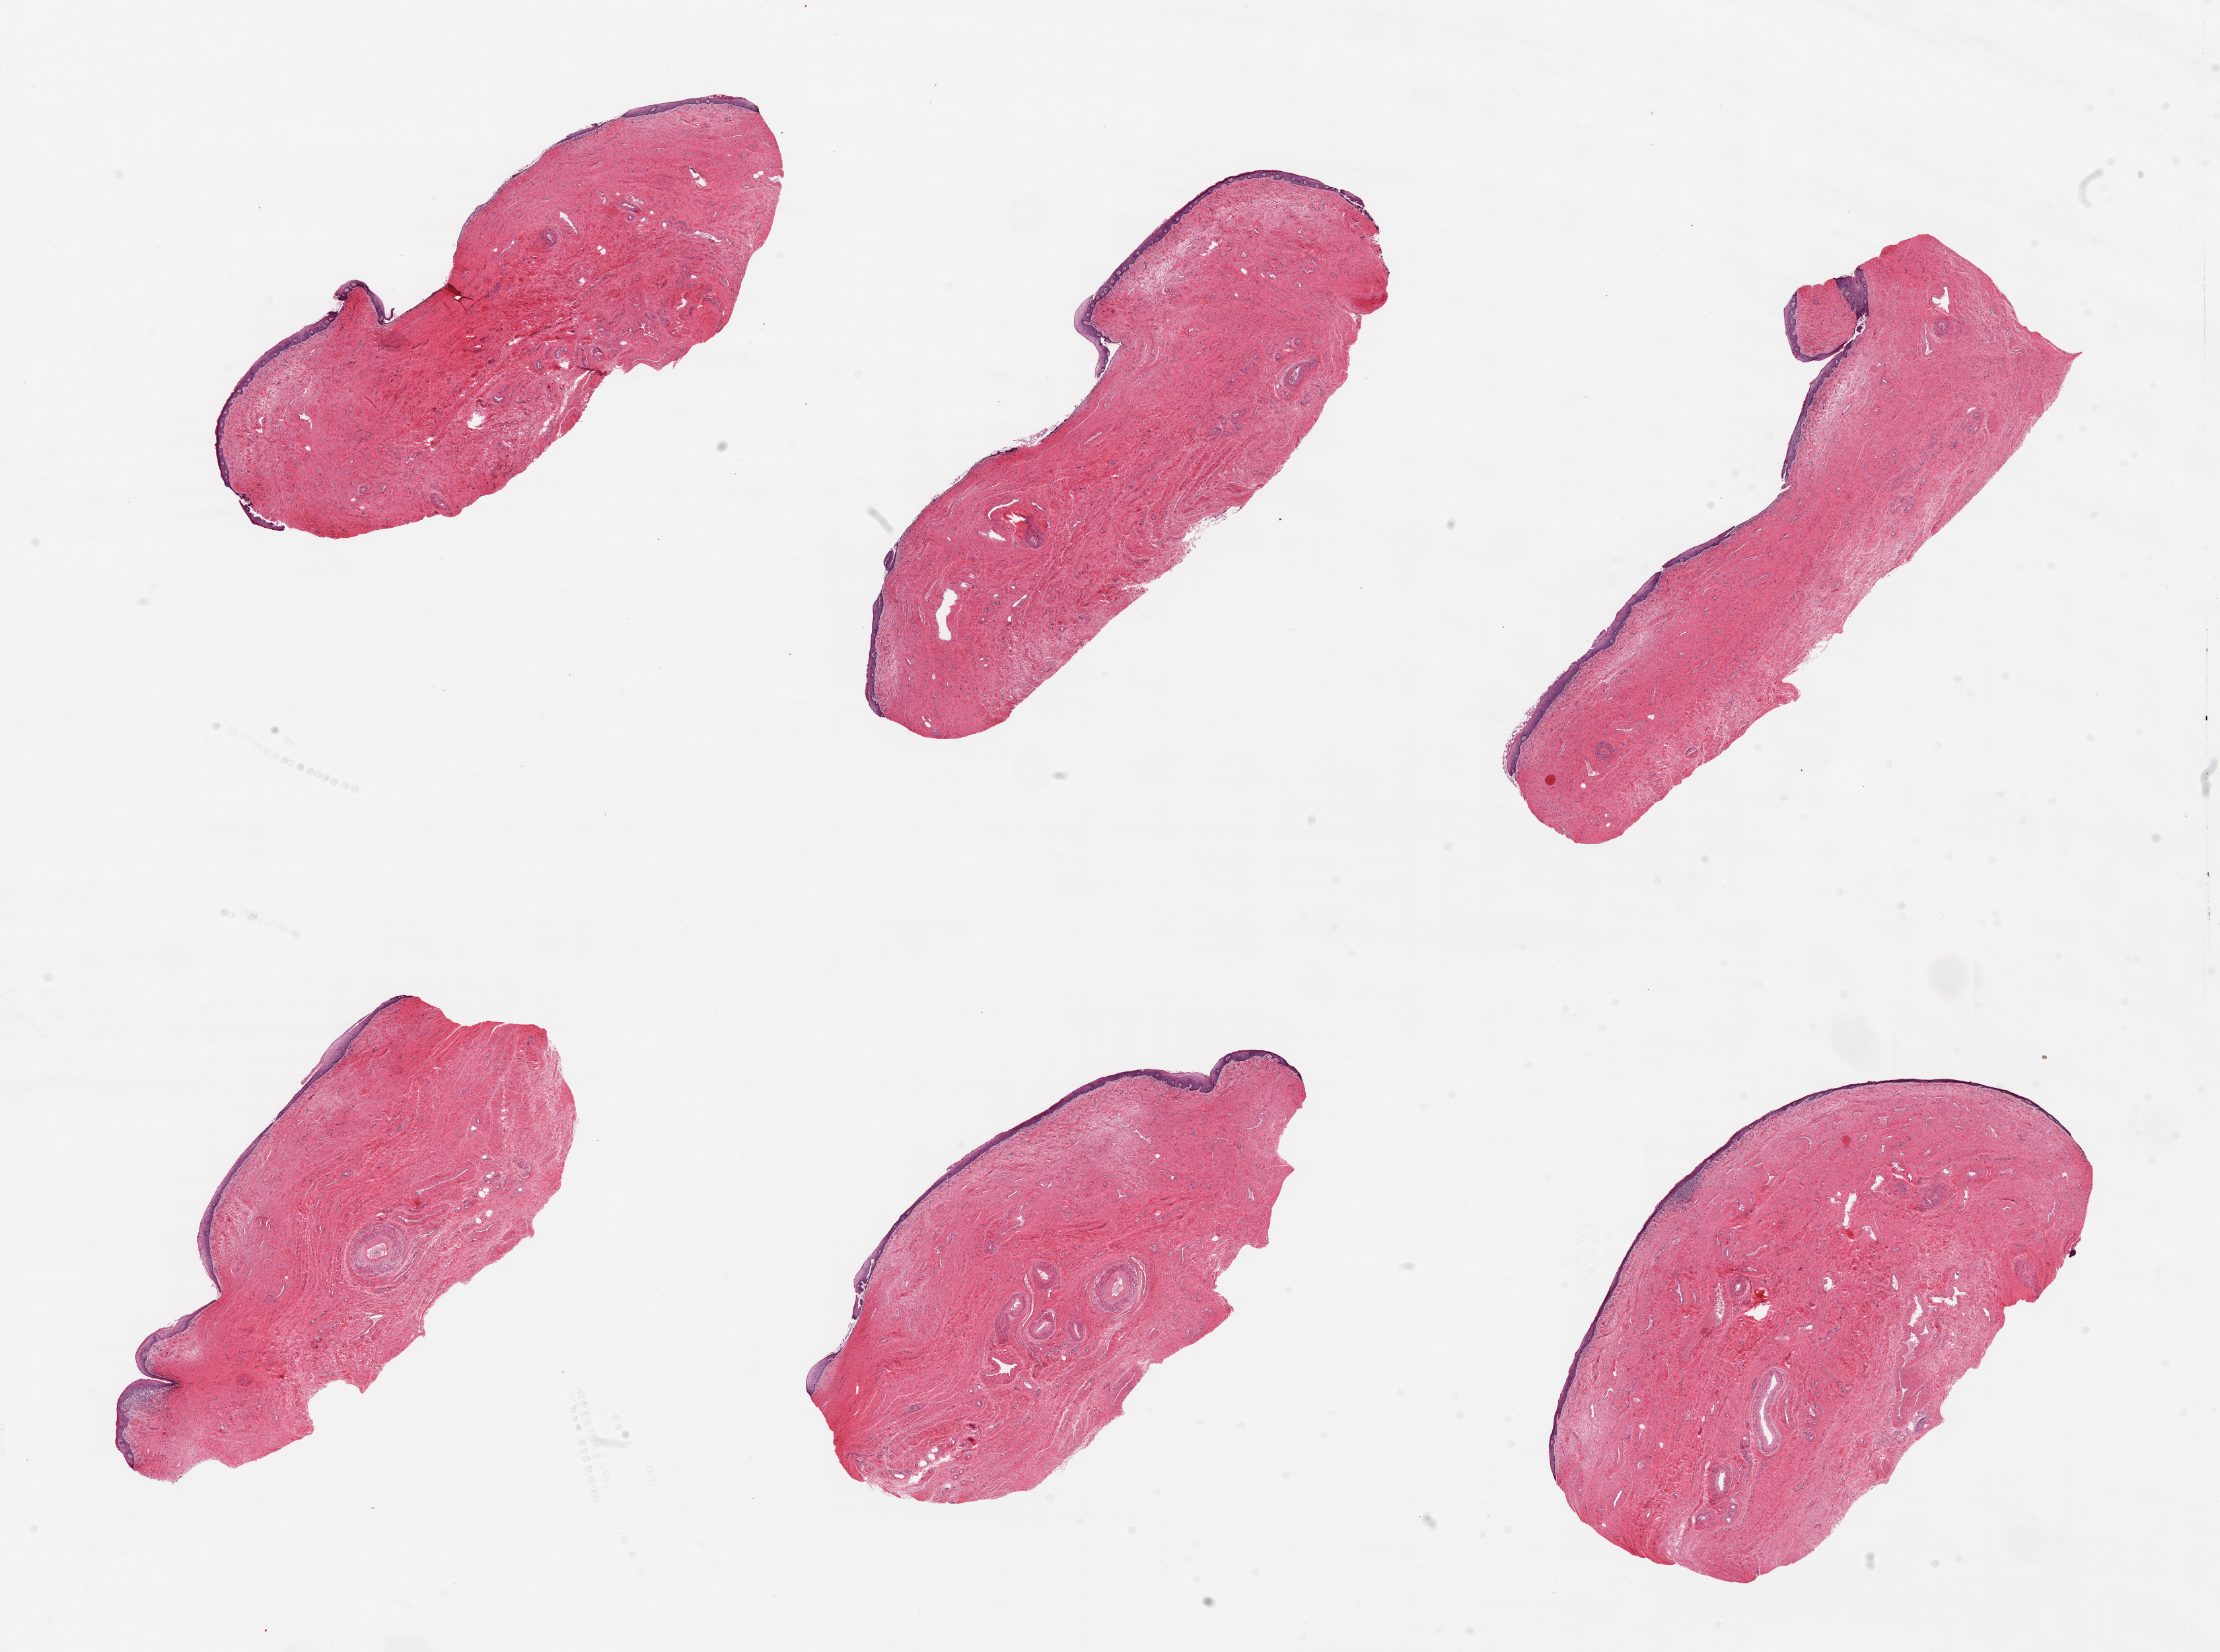
Hematoxylin and eosin (H&E) whole-slide image, low-resolution overview of the scanned area, about 26.6 x 19.8 mm. PAXgene-fixed, paraffin-embedded tissue. Section of vagina (target tissue). Tissue donor sample. Female donor.
Pathologist's review note for this sample: 6 pieces; atrophic epithelium.